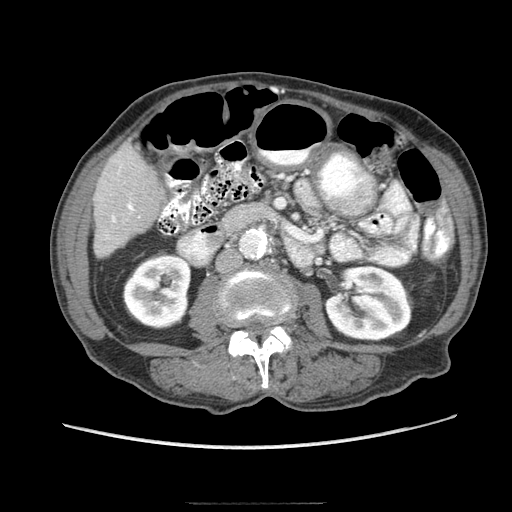
Contrast-enhanced abdominal CT (liver protocol), one axial slice. Position 22 of 83 along the scan axis. Soft-tissue window (W 400 / L 40 HU). 2.5 mm slice thickness. 512 × 512 image matrix, field of view 360 × 360 mm. From the clinical record (not read from this slice): diagnosis: hepatocellular carcinoma (patient treated with transarterial chemoembolisation; whether this scan precedes or follows treatment is not stated here); TNM stage (as recorded): Stage-I; Child-Pugh class: A; tumour differentiation: moderately differentiated.
Outlined on this slice (semi-automatic segmentation, software-assisted and operator-edited):
- liver parenchyma outside the tumour (the mass and vessels are separate outlines, so this box may not span the whole liver): bounding box <94,144,164,258> (left, top, right, bottom; pixels)
- liver vessels: <112,202,134,222>